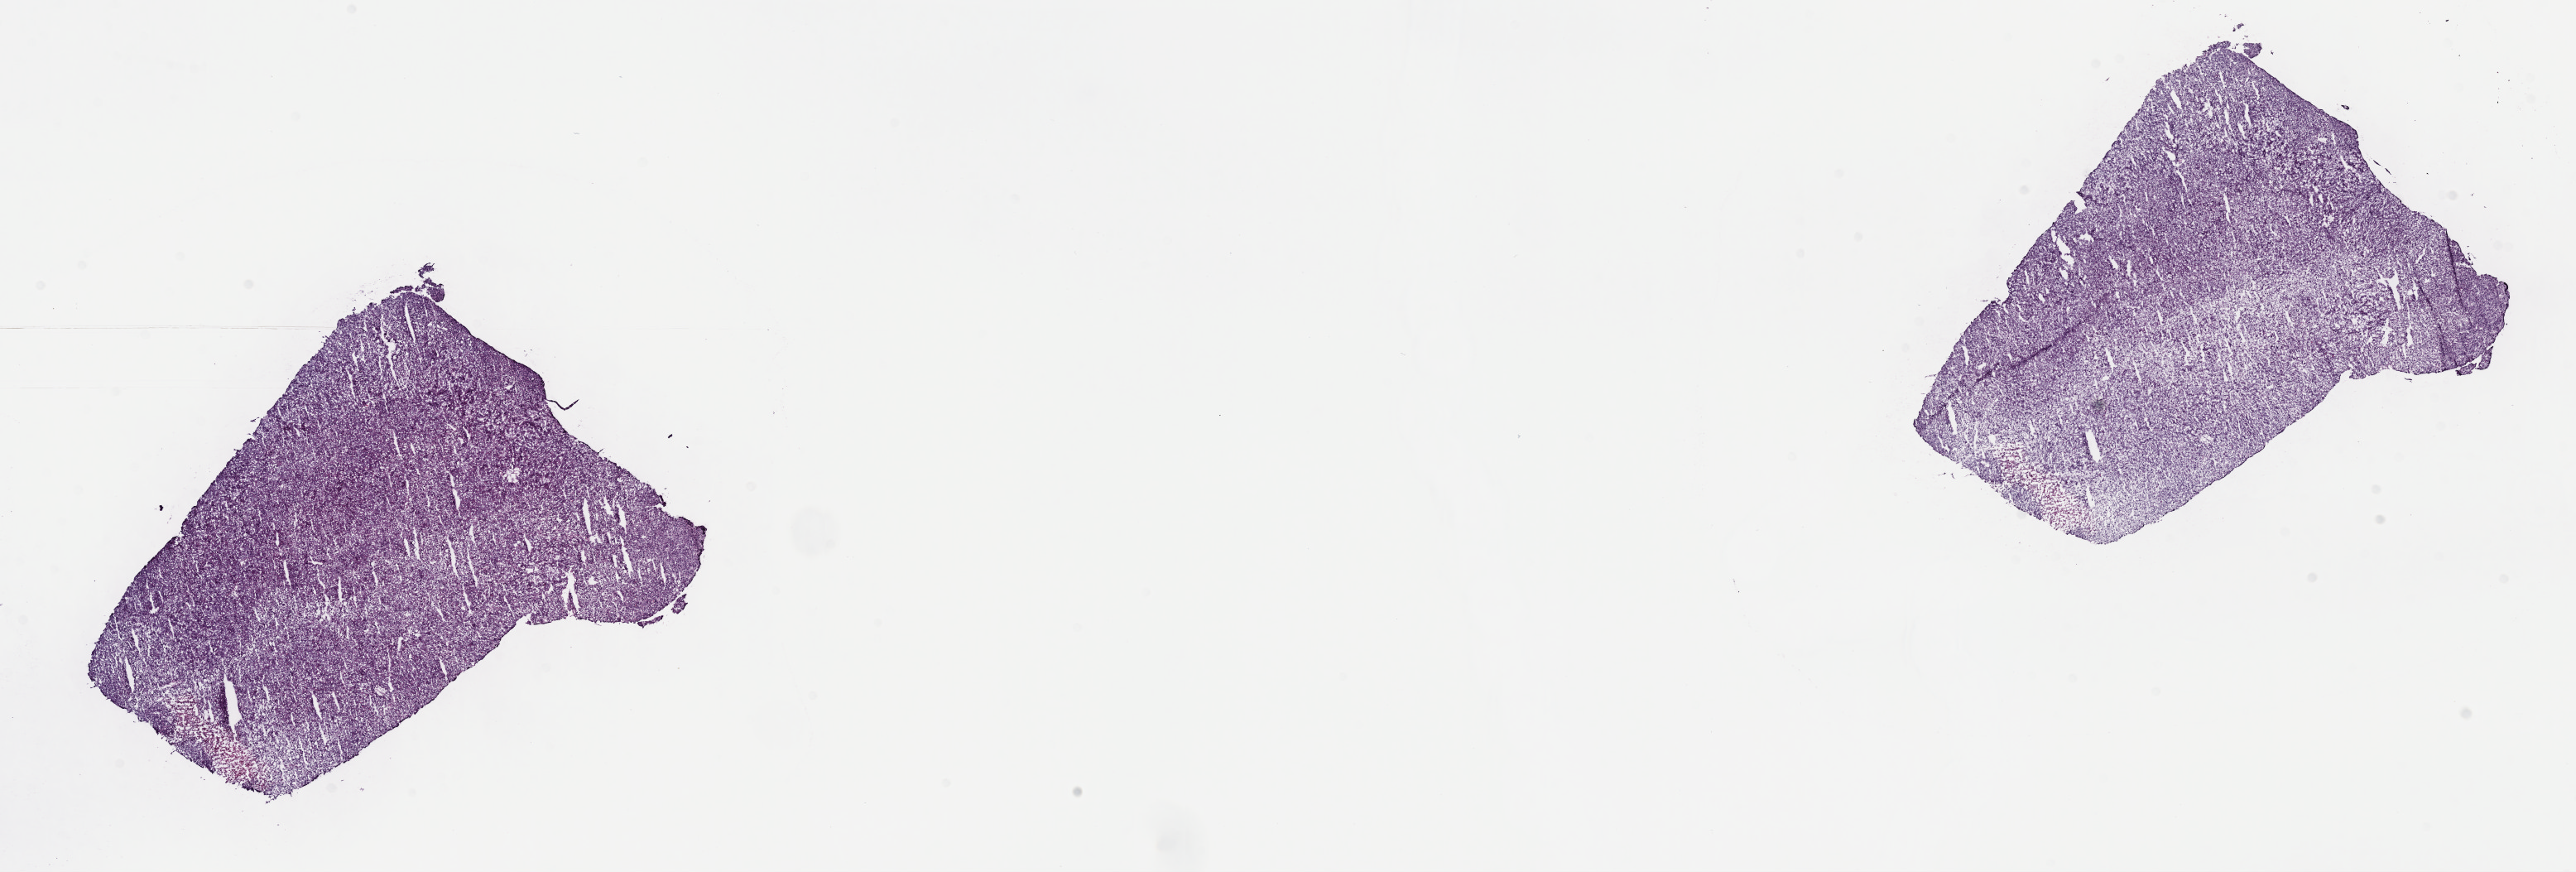
Digitized H&E tissue section (whole slide), low-resolution overview of the scanned area, about 25.2 x 8.5 mm (acquisition: 40x scan). Frozen section from the top of the tissue portion. Sample: primary tumour, liver. Male patient; age at initial diagnosis 66 years. Histologic grade: G3 (poorly differentiated). Composition of this section per pathologist review: tumour cells 92%, tumour nuclei 96%, normal cells 0%, stromal cells 3%, necrosis 5%. Infiltration values recorded for this section: lymphocyte infiltration 2%, monocyte infiltration 1%, neutrophil infiltration 0%.
Pathologic diagnosis: Hepatocellular carcinoma, NOS. AJCC pathologic stage: IIIA.